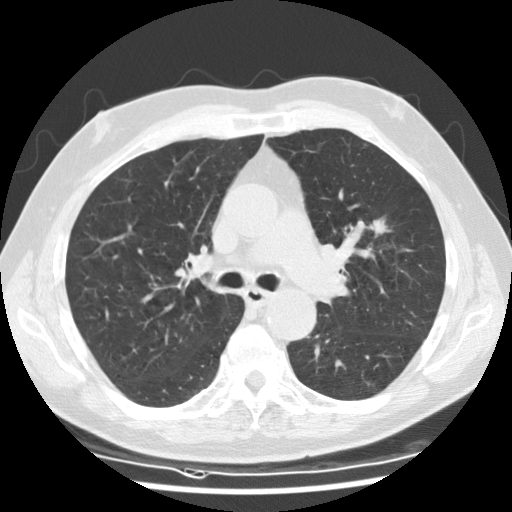
Low-dose screening chest CT, one axial slice. Position 80 of 135 along the scan axis. Reconstruction kernel STANDARD. 120 kVp. Lung window (W 1500 / L -600 HU). 2.5 mm slice thickness. 512 × 512 image matrix, field of view 340 × 340 mm.
Outlined on this slice (expert manual segmentation):
- lesion 1 (tumor, upper lobe of left lung): bounding box [x1, y1, x2, y2] px = [369, 218, 391, 238]